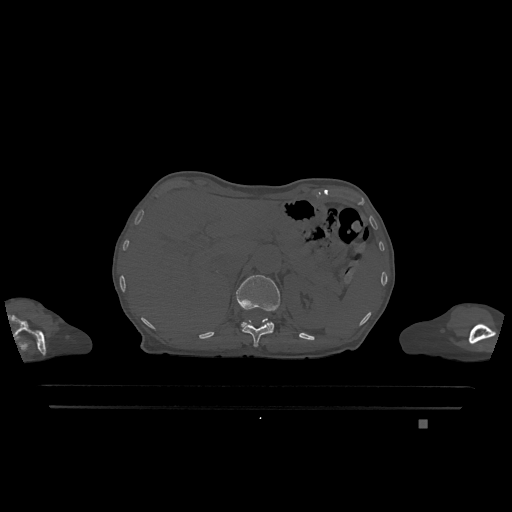
CT including the spine, one axial slice. Position 507 of 1317 along the scan axis. Bone window (W 1800 / L 400 HU). 0.5 mm slice thickness. 512 × 512 image matrix, field of view 500 × 500 mm. Patient: female, 74 years. Case-level facts recorded for this patient, not image findings: primary cancer: lung.
Outlined on this slice (semi-automatic segmentation, software-assisted and operator-edited):
- L1 vertebra: bounding box <236,275,280,332> (left, top, right, bottom; pixels)
- T12 vertebra: <242,318,272,347>